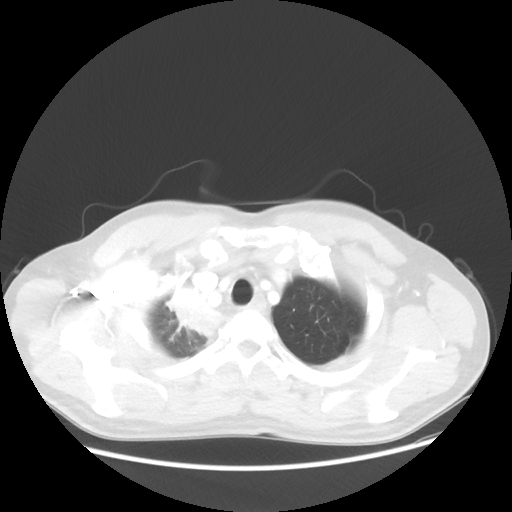
Chest CT, one axial slice; slice 48 of 56 in the series (ordered by position); 100 kVp; lung window (W 1500 / L -600 HU); 512 × 512 image matrix, field of view 398 × 398 mm. Patient: male, 60 years. From the clinical record (not read from this slice): clinical TNM (as recorded): T2a N1 M0.
Outlined on this slice (bounding box drawn by a radiologist):
- lung tumour (recorded histology: squamous cell carcinoma): bounding box [x1, y1, x2, y2] px = [162, 276, 231, 345]